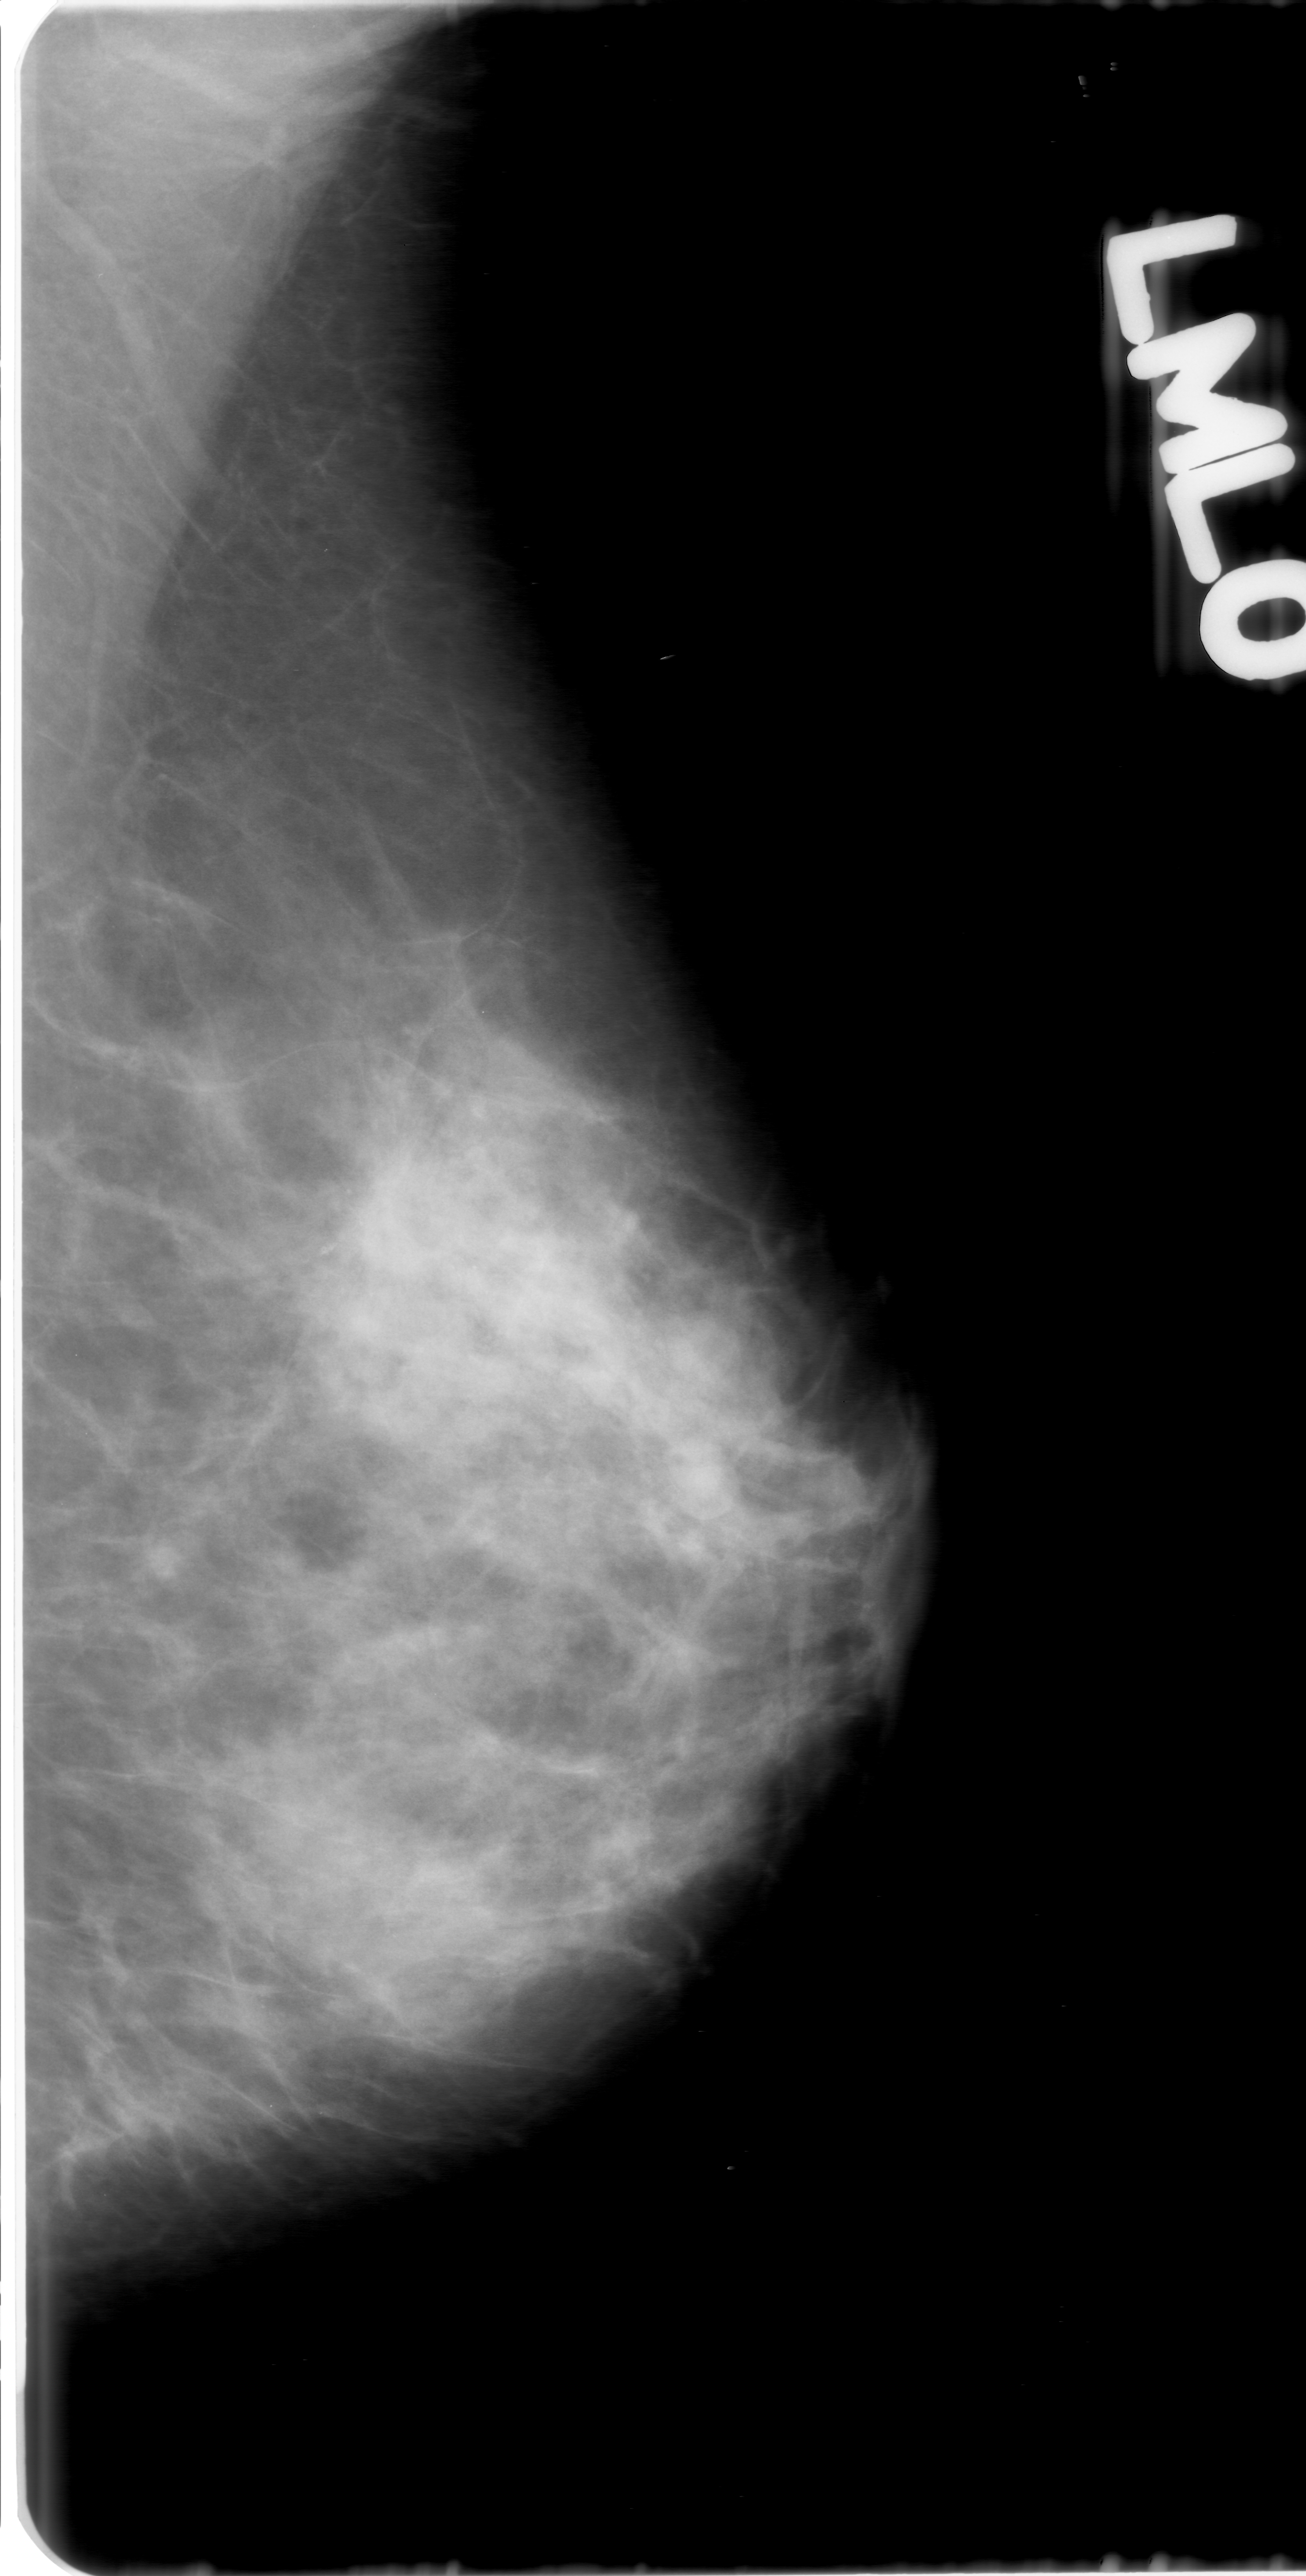
Digitized screen-film mammogram, left breast, MLO view.
Marked findings (only marked abnormalities are described; nothing is implied about the rest of the image): calcifications, morphology amorphous, distribution clustered; BI-RADS assessment category 3; pathology result (as recorded, not read from the image): malignant.